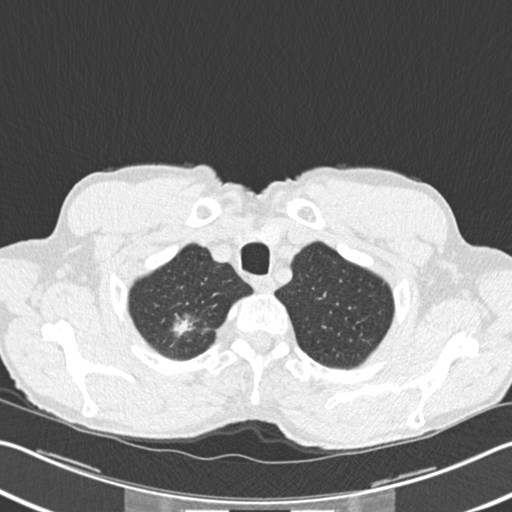
Low-dose screening chest CT, axial slice. Second annual screen. Lung window (W 1500 / L -600 HU). 2 mm slice thickness. Standard (soft-tissue) reconstruction kernel (B30f). Slice 21 of 220 in the series. 512 × 512 image matrix, field of view 342 × 342 mm. Male participant, aged 62 years at enrolment. Former smoker at enrolment.
Lesion marked by an expert reader, box from (x=162, y=305) to (x=207, y=349) px. The screening reader recorded 2 non-calcified nodules or masses ≥4 mm on this exam; which of them this box marks is not recorded. Official screen result: positive, change unspecified: nodule(s) >= 4 mm or enlarging nodule(s), mass(es), or other non-specific abnormalities suspicious for lung cancer. Later outcome: lung cancer diagnosed 5 days after this screen — bronchiolo-alveolar adenocarcinoma, NOS, right upper lobe, well differentiated (G1), stage IA (AJCC 6th edition), 15 mm at pathology.